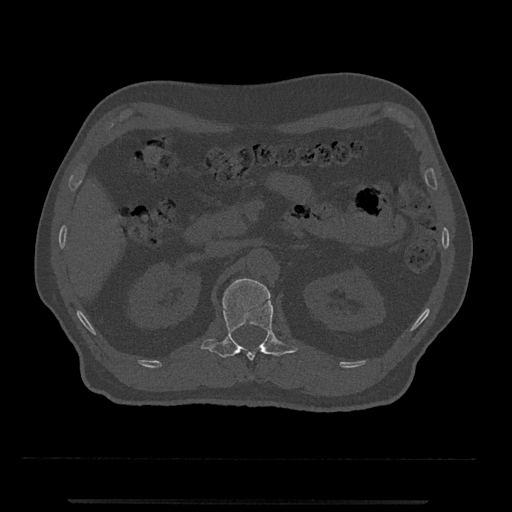
CT including the spine, one axial slice. Slice 341 of 797 in the series (ordered by position). Reconstruction kernel Br40s/3. Bone window (W 1800 / L 400 HU). 0.5 mm slice thickness. 512 × 512 image matrix, field of view 419 × 419 mm. Patient: male, 63 years. From the clinical record (not read from this slice): primary cancer: prostate.
Outlined on this slice (semi-automatically segmented with operator editing):
- L1 vertebra: box from (x=201, y=278) to (x=298, y=361) px